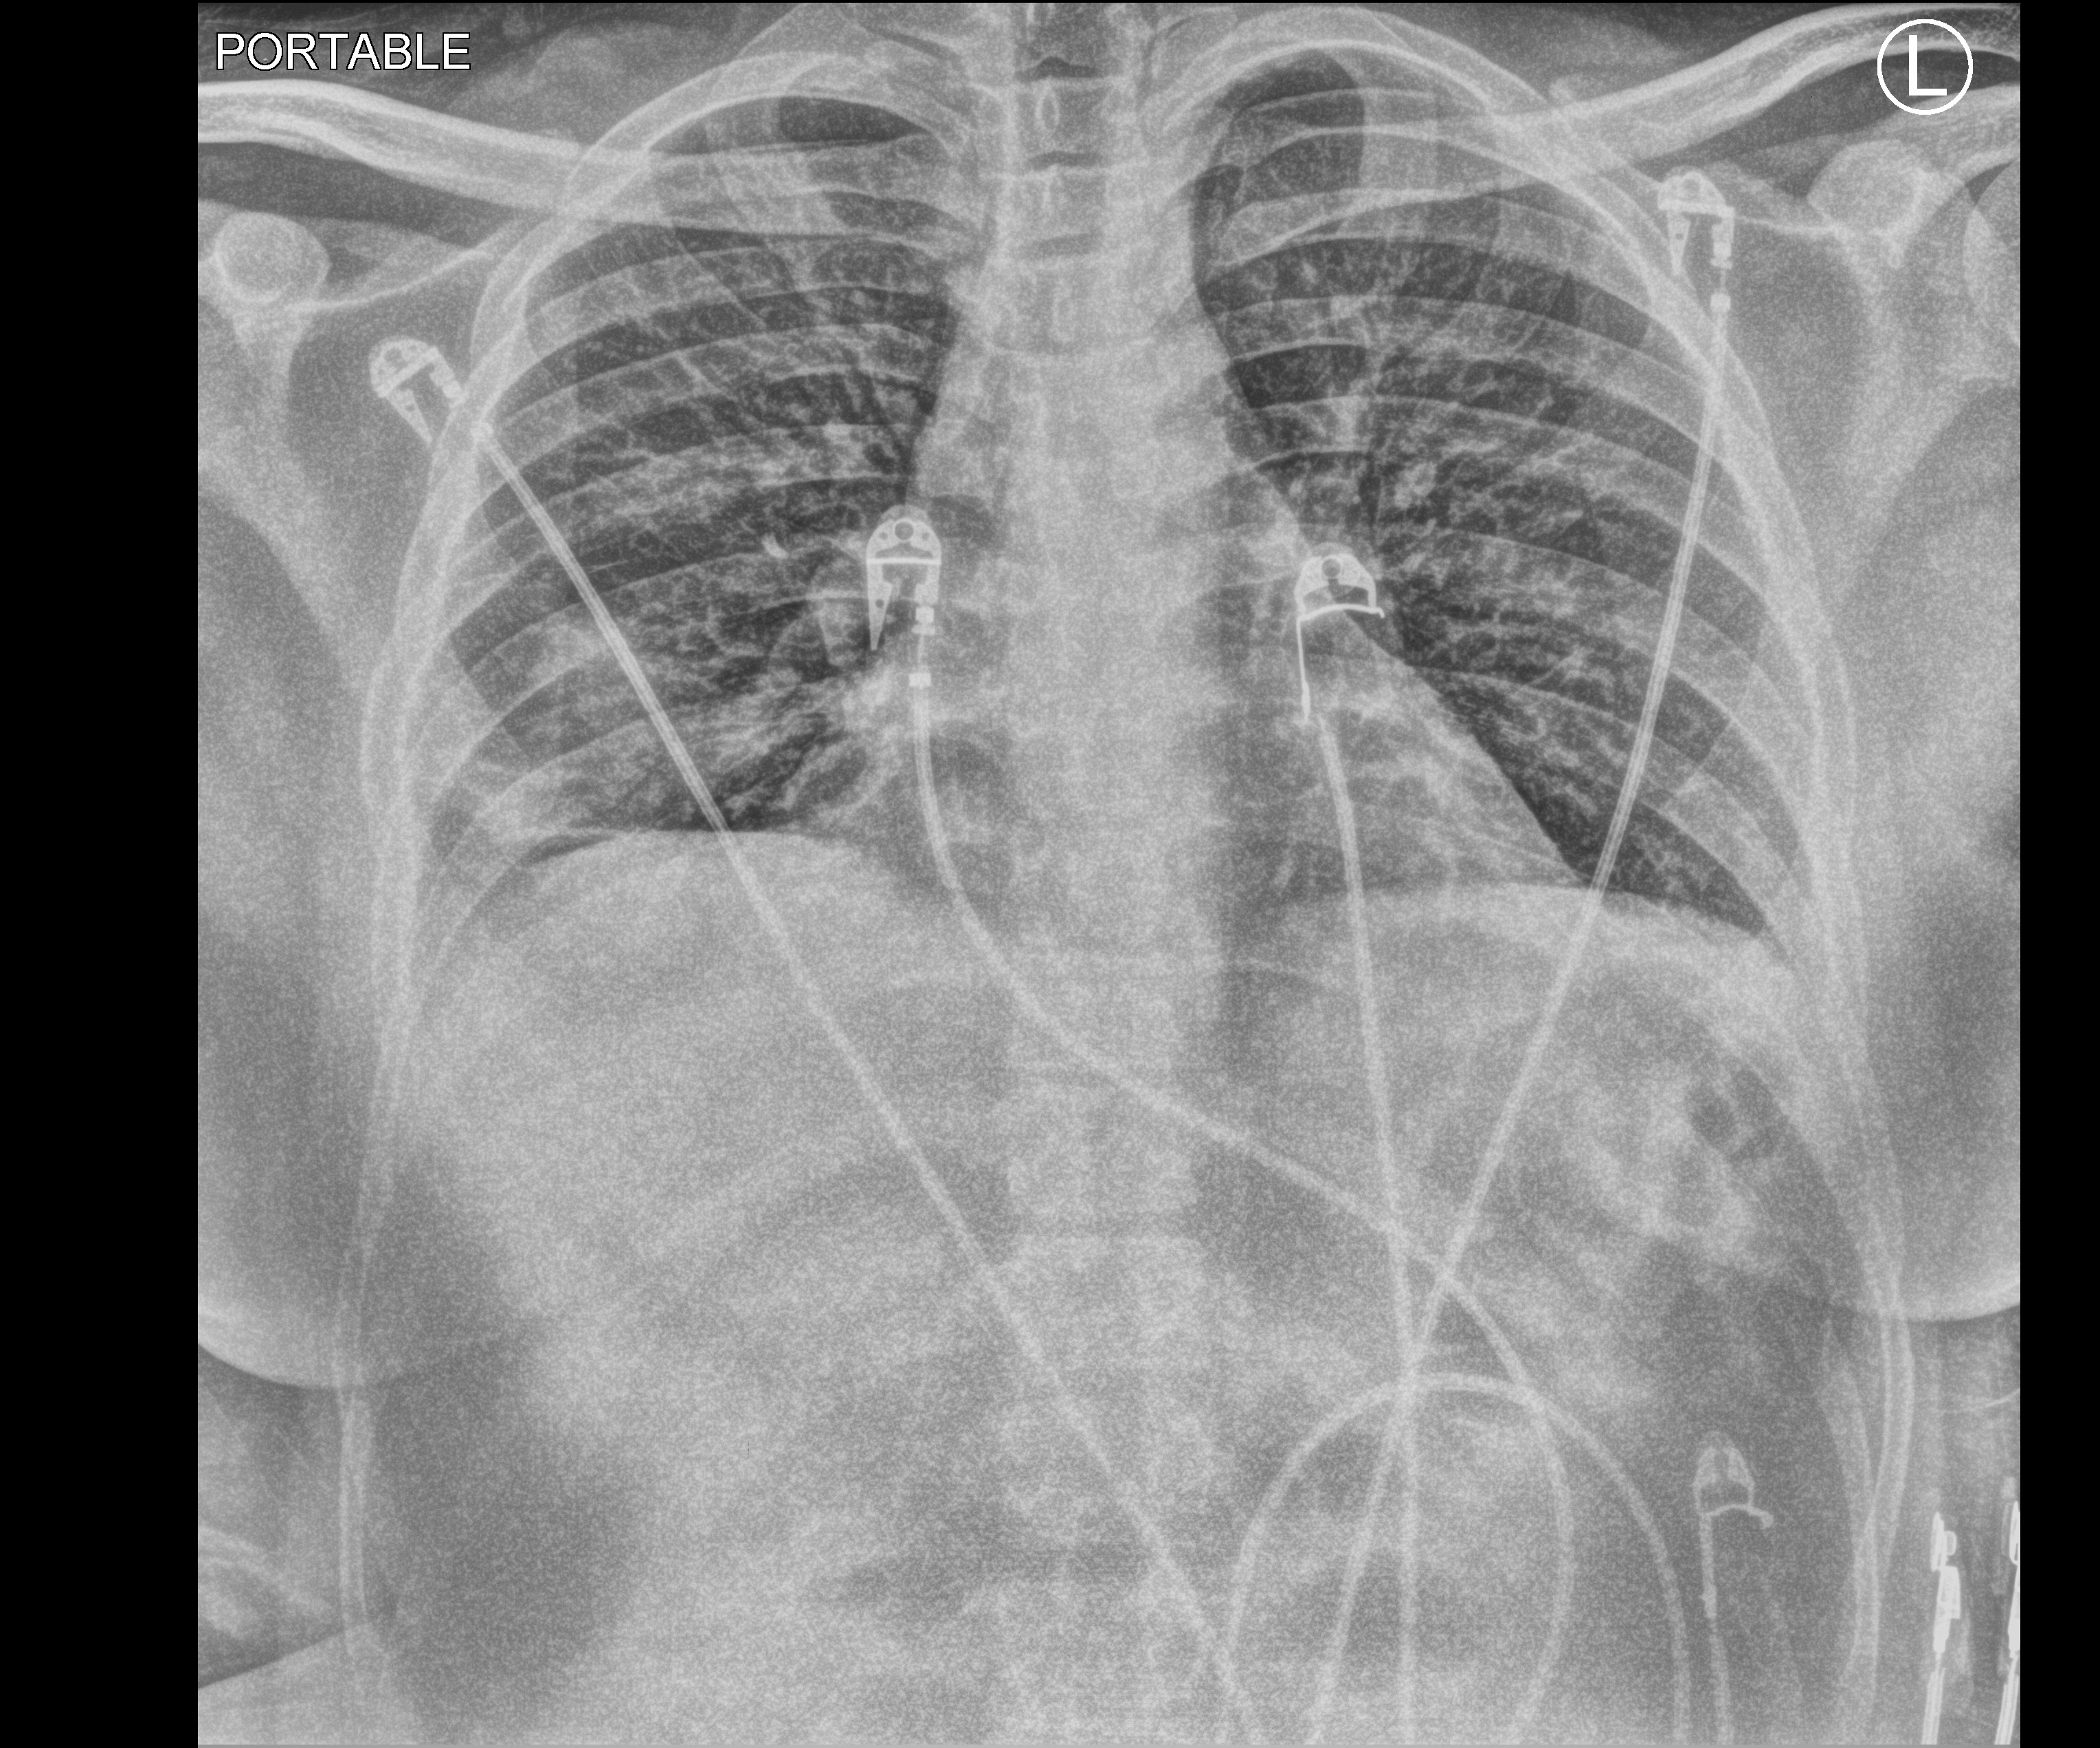
Chest X-ray (portable). Patient hospitalised with COVID-19; male, aged 18–59 years.
From the hospital-stay record, not from the radiograph (when in the stay this image was taken is not recorded): mechanically ventilated during this hospital stay: no; admitted to intensive care during this hospital stay: no.